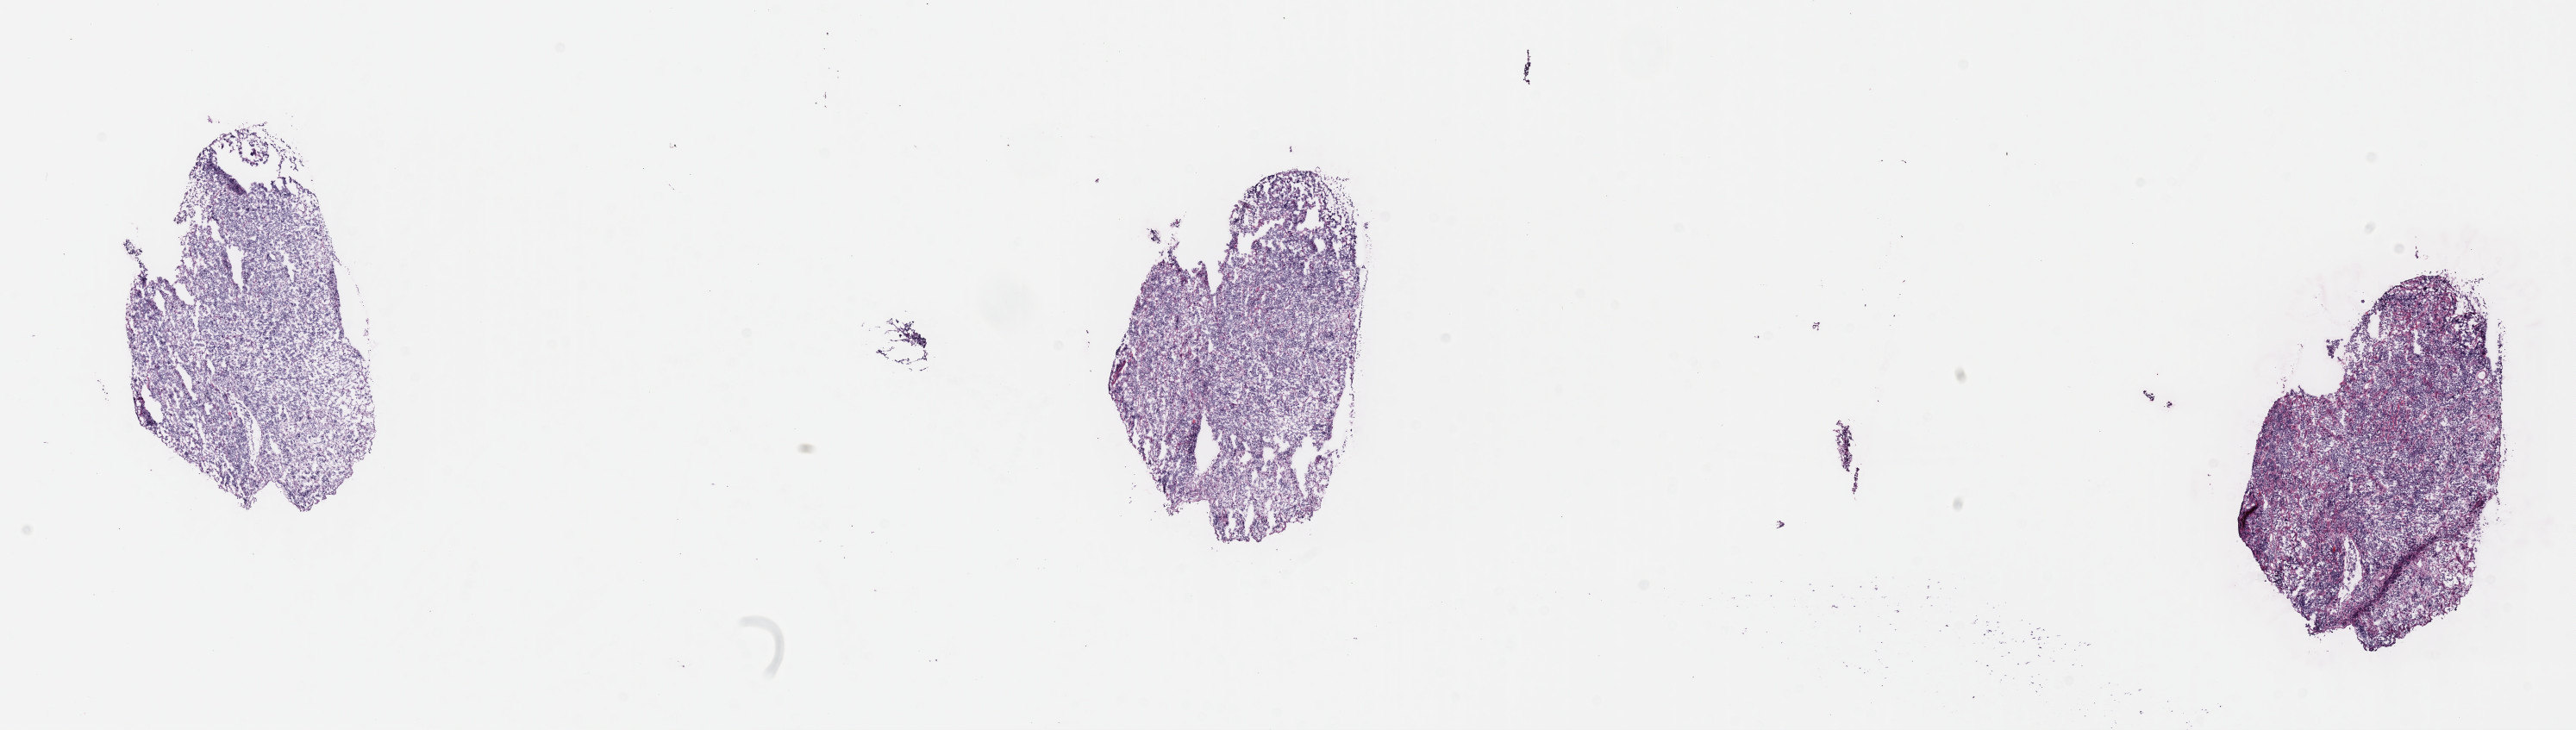
Hematoxylin and eosin (H&E) whole-slide image, shown as a low-resolution overview of the whole scanned area (about 24.1 x 6.8 mm), frozen section, specimen: primary tumor, site: cranium. Patient: male, age at initial diagnosis 7 years. Slide review estimates, as recorded: tumor cells 80%, tumor nuclei 90%, stromal cells 10%, necrosis 5%, normal cells 5%. Inflammatory infiltration, as recorded: lymphocyte infiltration 10%, monocyte infiltration 10%, neutrophil infiltration 0%.
Ann Arbor stage (patient): Stage III. Histologic diagnosis: Burkitt lymphoma, NOS.